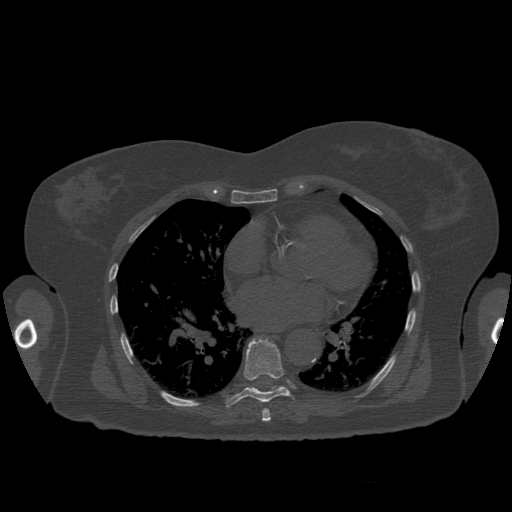
CT including the spine, one axial slice. Slice 377 of 399 in the series (ordered by position). Reconstruction kernel STANDARD. Bone window (W 1800 / L 400 HU). 1.25 mm slice thickness. 512 × 512 image matrix, field of view 404 × 404 mm. Patient age 81 years. From the clinical record (not read from this slice): primary cancer: renal.
Structures marked on this image (semi-automatically segmented with operator editing):
- T7 vertebra: box from (x=262, y=408) to (x=271, y=422) px
- T8 vertebra: (x=226, y=338)–(x=291, y=408)